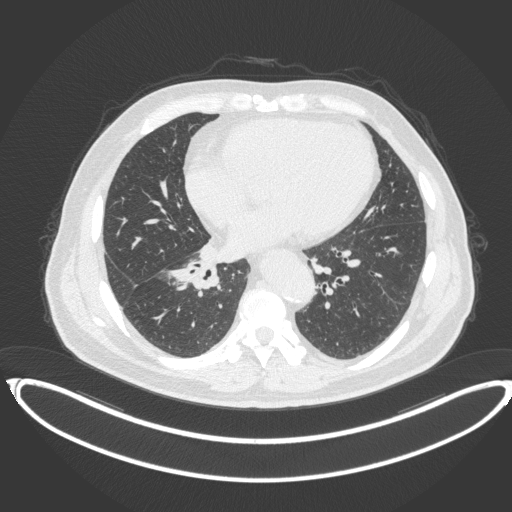
Chest CT, one axial slice. Slice 167 of 383 in the series (ordered by position). Reconstruction kernel B31f. Lung window (W 1500 / L -600 HU). 1 mm slice thickness. 512 × 512 image matrix, field of view 448 × 448 mm. Male patient, age 61 years. From the clinical record (not read from this slice): clinical TNM (as recorded): T1b N1 M0.
Annotated regions visible in this slice (bounding box drawn by a radiologist):
- lung tumour (recorded histology: squamous cell carcinoma): bounding box <182,259,220,291> (left, top, right, bottom; pixels)